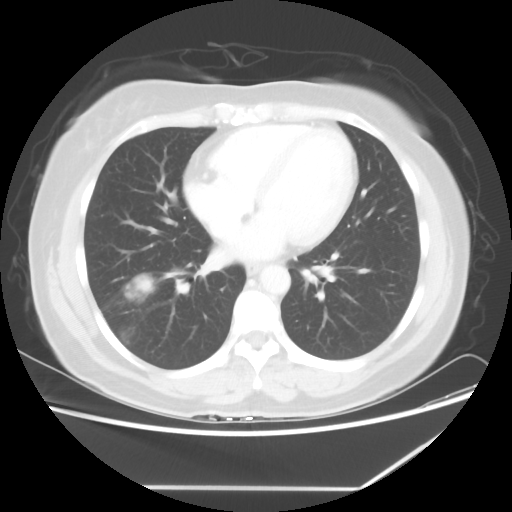
Chest CT, one axial slice. Slice 26 of 60 in the series (ordered by position). Reconstruction kernel STANDARD. 100 kVp. Lung window (W 1500 / L -600 HU). 5 mm slice thickness. 512 × 512 image matrix. Female patient, age 42 years. Case-level facts recorded for this patient, not image findings: clinical TNM (as recorded): T2 N1 M0.
Annotated regions visible in this slice (bounding box drawn by a radiologist):
- lung tumour (recorded histology: adenocarcinoma): bounding box (x1, y1, x2, y2) in pixels: (130, 274, 155, 292)